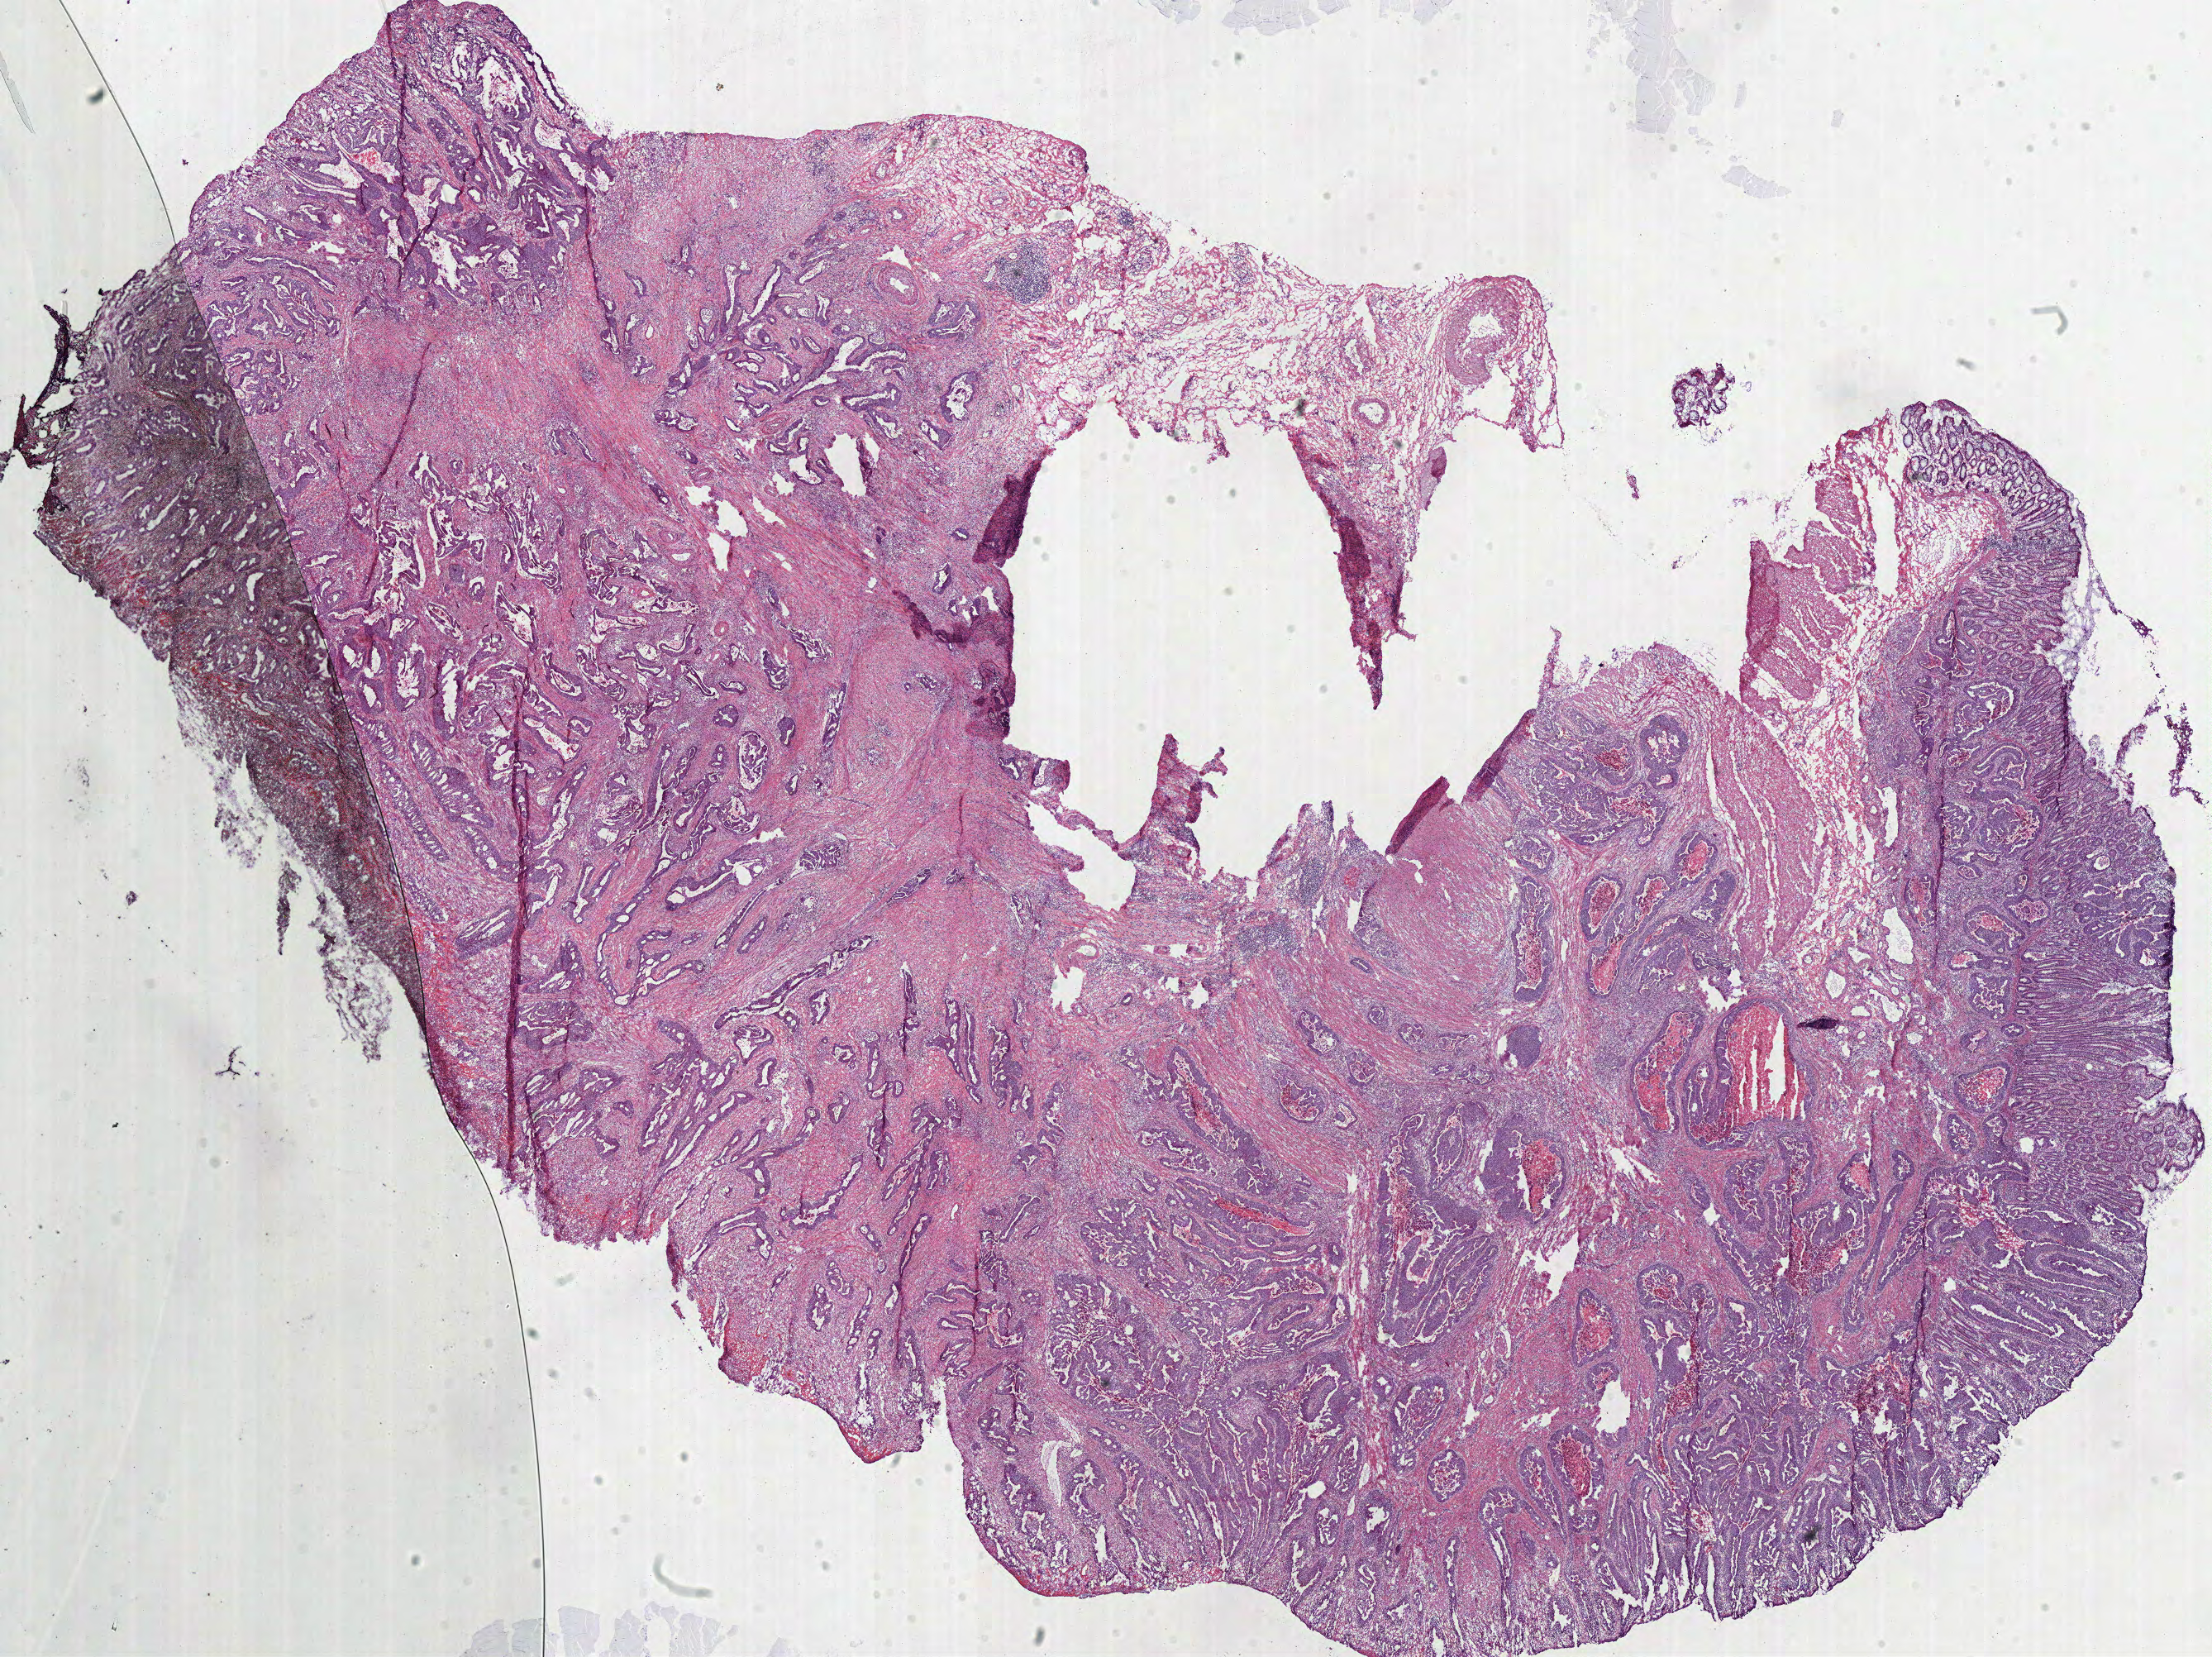
Digitized Hematoxylin and eosin (H&E) stained tissue section (whole slide) — a low-resolution overview of the entire scanned area, about 21.0 x 15.8 mm (from a 40x scan); frozen section from the bottom of the tissue portion; colon, primary tumour sample. Patient: male, age at initial diagnosis 60 years. Slide review estimates, as recorded: tumour cells 45%, tumour nuclei 70%, normal cells 10%, stromal cells 30%, necrosis 15%.
Diagnosis: Adenocarcinoma, NOS. AJCC pathologic stage: I. Lymph nodes positive (case pathology): 0 of 19 examined.